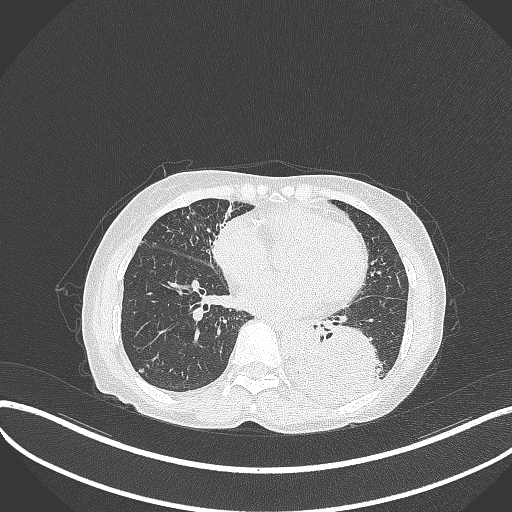
Chest CT, one axial slice. Slice 118 of 370 in the series (ordered by position). Reconstruction kernel B70f. Lung window (W 1500 / L -600 HU). 512 × 512 image matrix, field of view 400 × 400 mm. Female patient, age 78 years. Case-level facts recorded for this patient, not image findings: clinical TNM (as recorded): T3 N0 M1.
Structures marked on this image (bounding box drawn by a radiologist):
- lung tumour (recorded histology: squamous cell carcinoma): bounding box (x1, y1, x2, y2) in pixels: (290, 318, 384, 407)